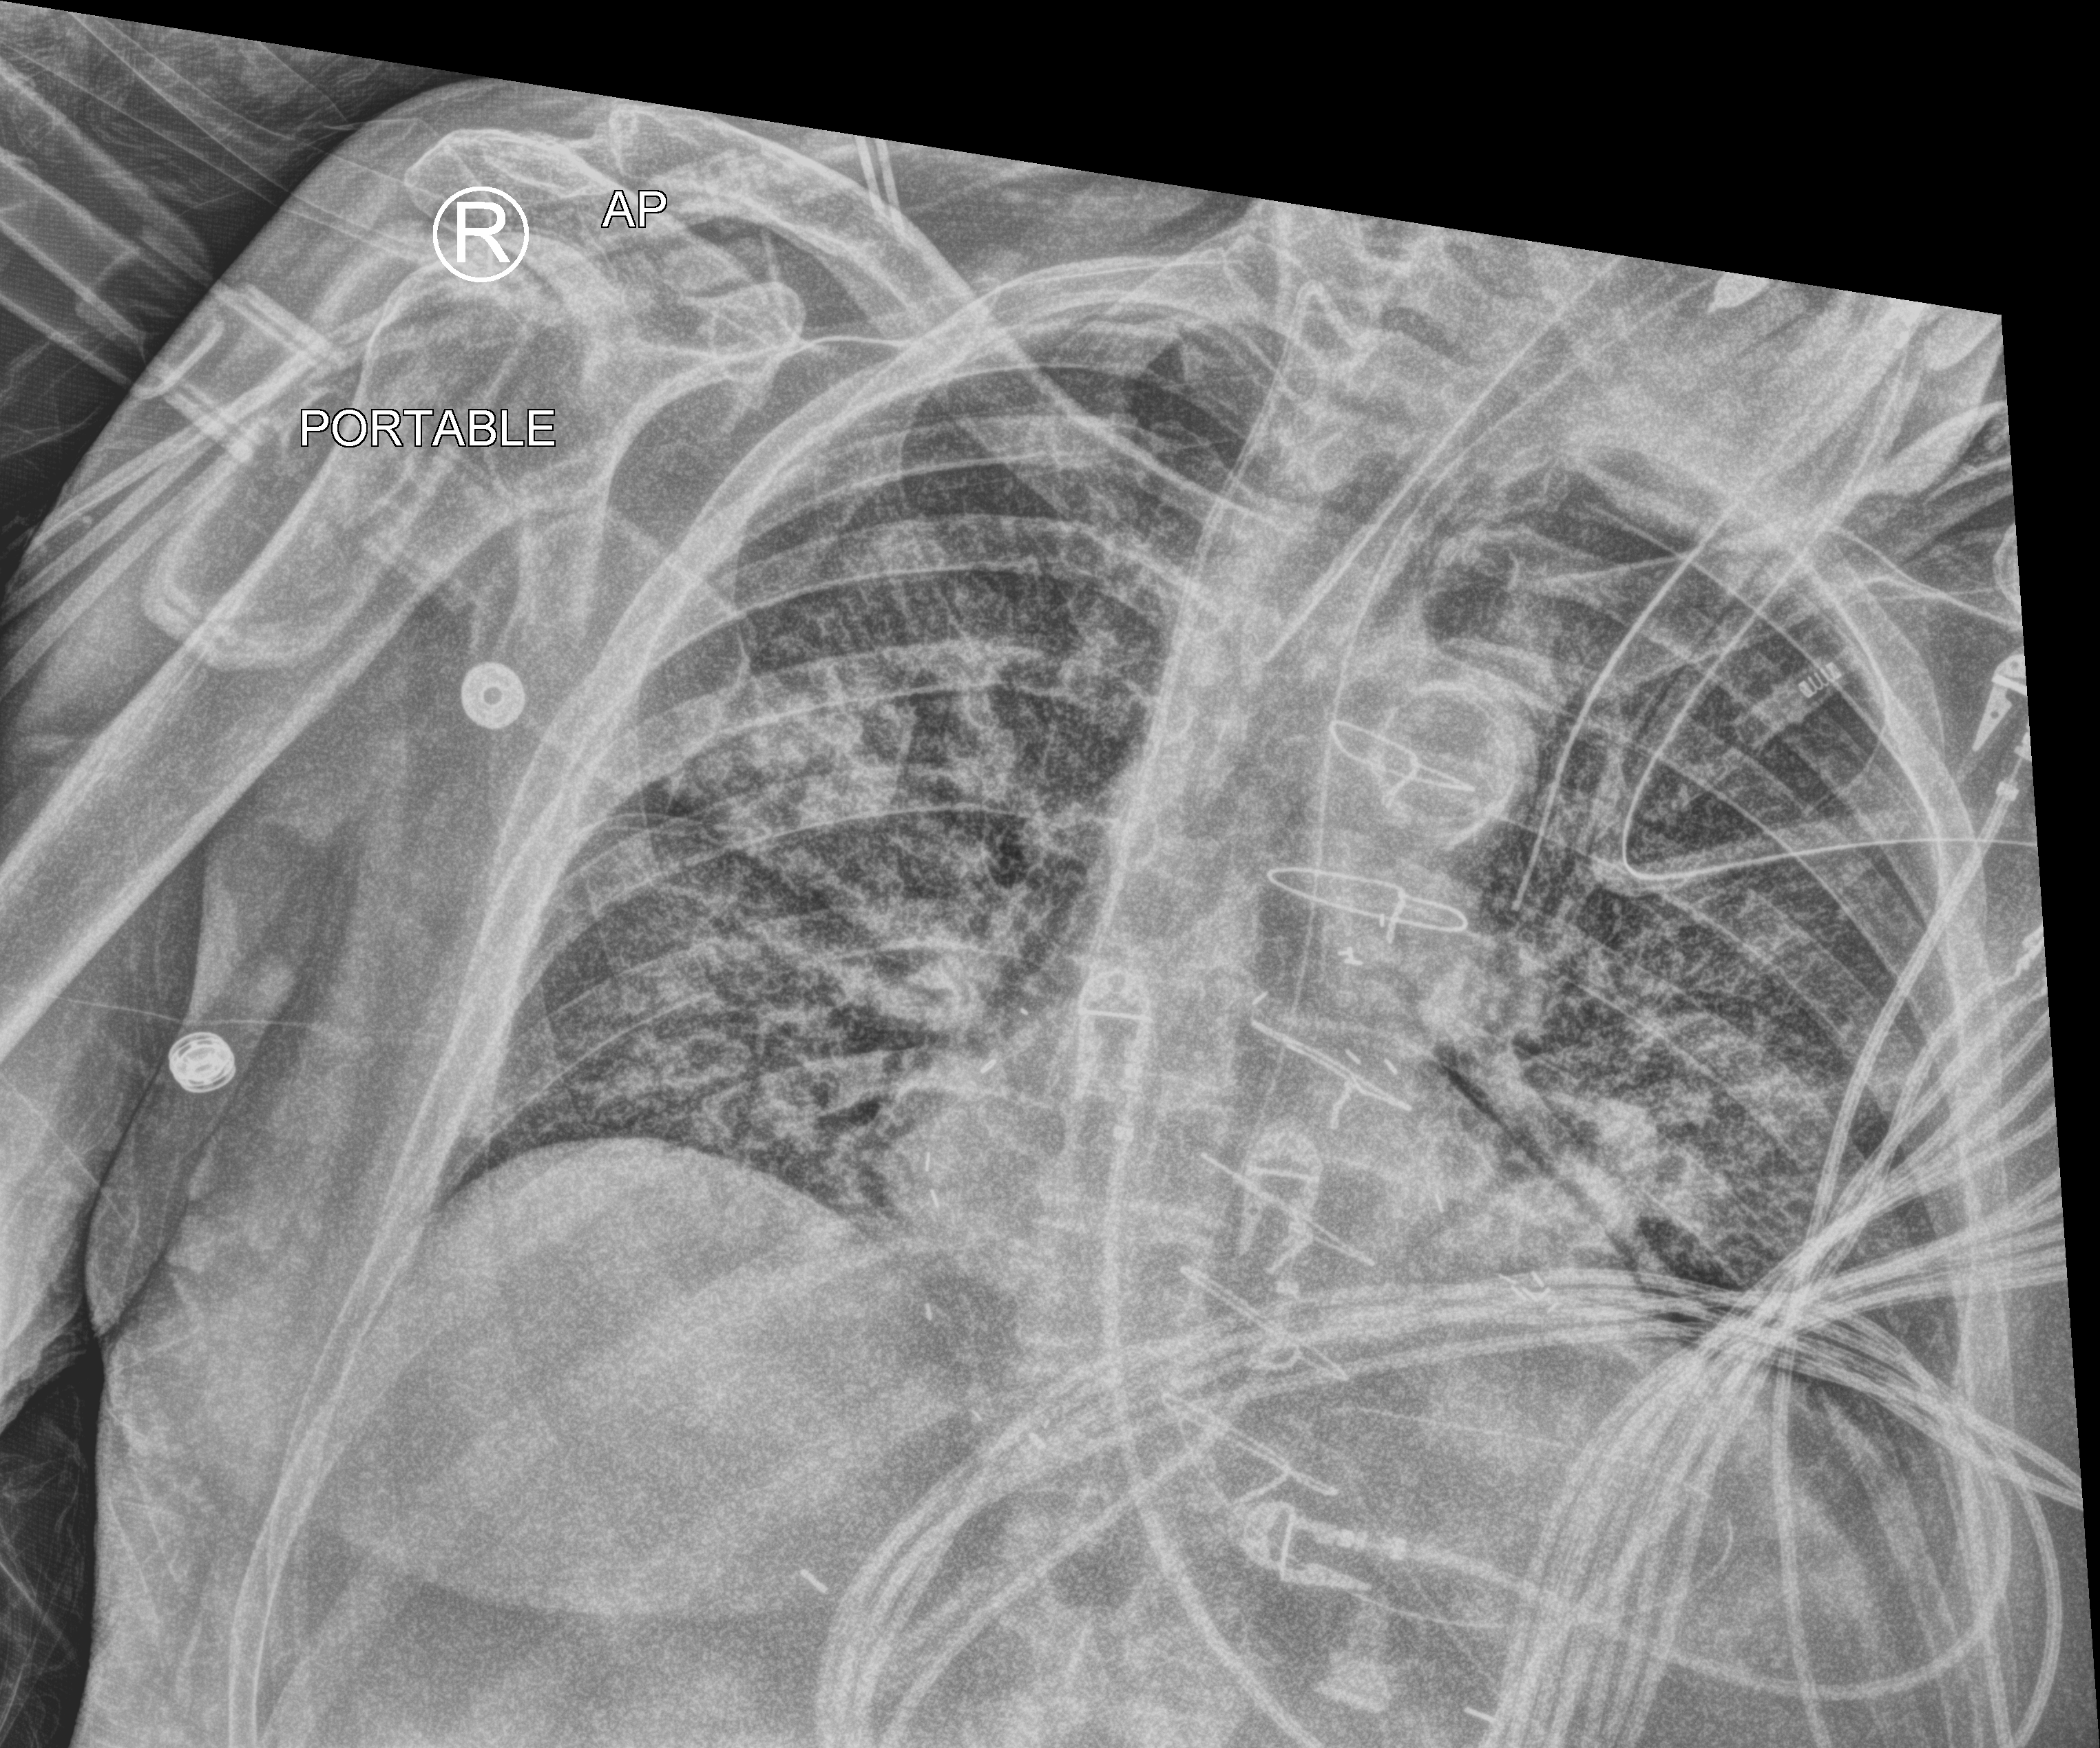
Bedside chest radiograph (computed radiography); anteroposterior (AP) projection. Patient hospitalised with COVID-19; male, aged 75–90 years.
Hospital-stay facts (about this admission, not read from this image; timing relative to this image not recorded): admitted to intensive care during this hospital stay: yes.